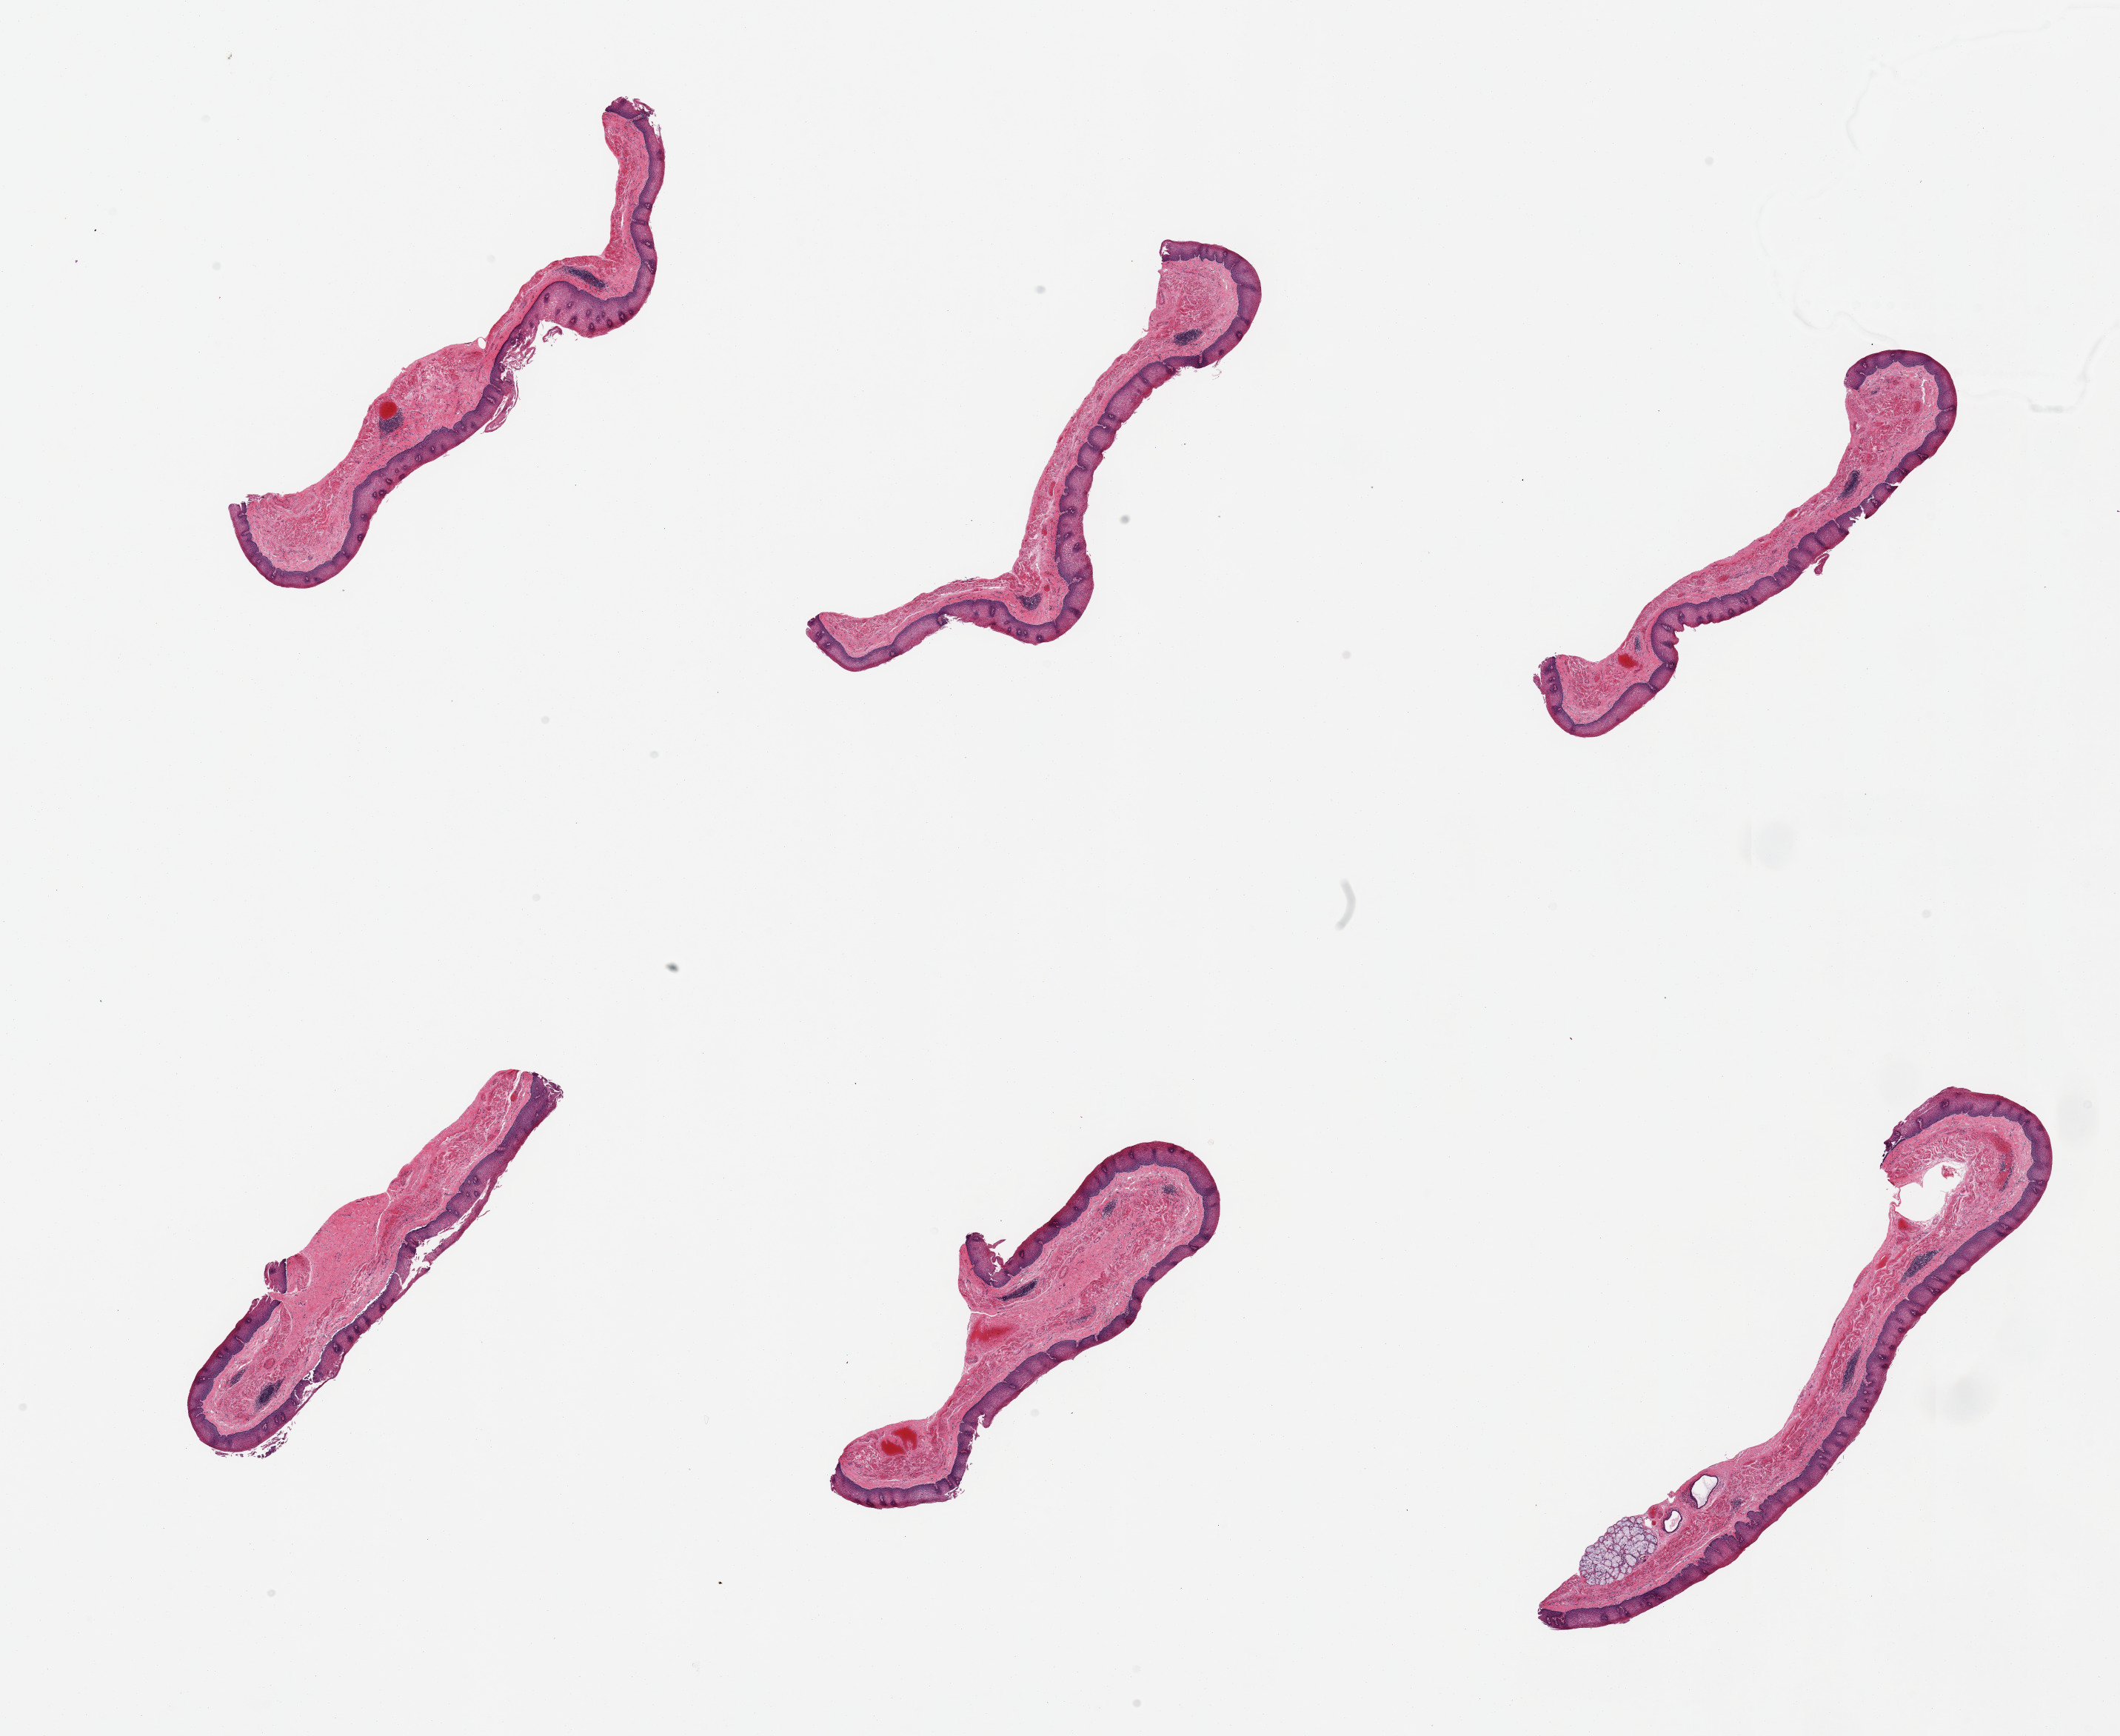
Whole-slide image, H&E stain, a low-resolution overview of the entire scanned area, about 22.6 x 18.5 mm (acquisition: 20x scan). PAXgene-fixed paraffin-embedded (PFPE) section. Sampled site (target tissue): esophageal mucous membrane. Tissue donor sample. Donor sex: male.
- review note (as recorded): 6 pieces, squamous mucosa is ~0.25mm, 40-50% thickness